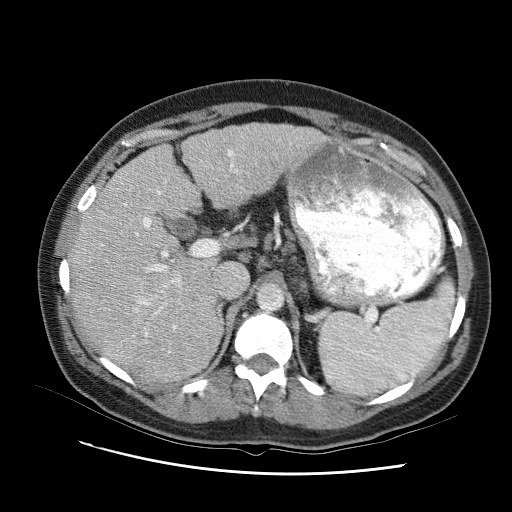
Contrast-enhanced abdominal CT (liver protocol), one axial slice. Slice 61 of 95 in the series (ordered by position). Reconstruction kernel STANDARD. One of 2 acquisitions stored at this slice position. Soft-tissue window (W 400 / L 40 HU). 2.5 mm slice thickness. 512 × 512 image matrix, field of view 360 × 360 mm. Case-level facts recorded for this patient, not image findings: diagnosis: hepatocellular carcinoma (patient treated with transarterial chemoembolisation; whether this scan precedes or follows treatment is not stated here); TNM stage (as recorded): Stage-I; Child-Pugh class: B; tumour nodularity: uninodular.
Annotated regions visible in this slice (semi-automatically segmented with operator editing):
- abdominal aorta: box from (x=257, y=283) to (x=282, y=309) px
- liver parenchyma outside the tumour (the mass and vessels are separate outlines, so this box may not span the whole liver): (x=68, y=118)–(x=330, y=376)
- liver vessels: (x=105, y=139)–(x=293, y=348)